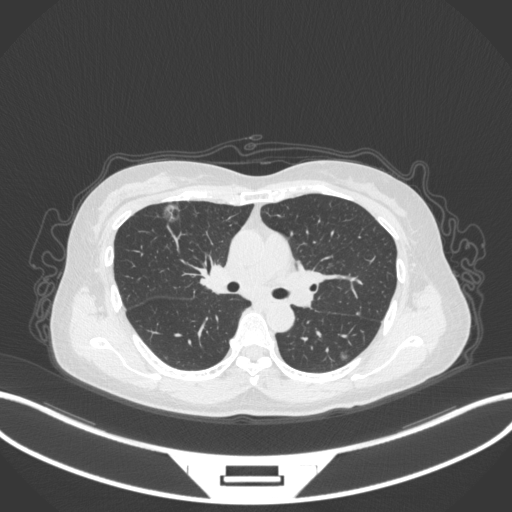
Chest CT, one axial slice; position 200 of 317 along the scan axis; lung window (W 1500 / L -600 HU); 512 × 512 image matrix, field of view 400 × 400 mm. Patient: female, 61 years. Case-level facts recorded for this patient, not image findings: clinical TNM (as recorded): T1b N0 M0; histopathological grade: G1.
Annotated regions visible in this slice (rectangle marked by the reading radiologist):
- lung tumour (recorded histology: adenocarcinoma): bounding box (x1, y1, x2, y2) in pixels: (162, 201, 183, 227)